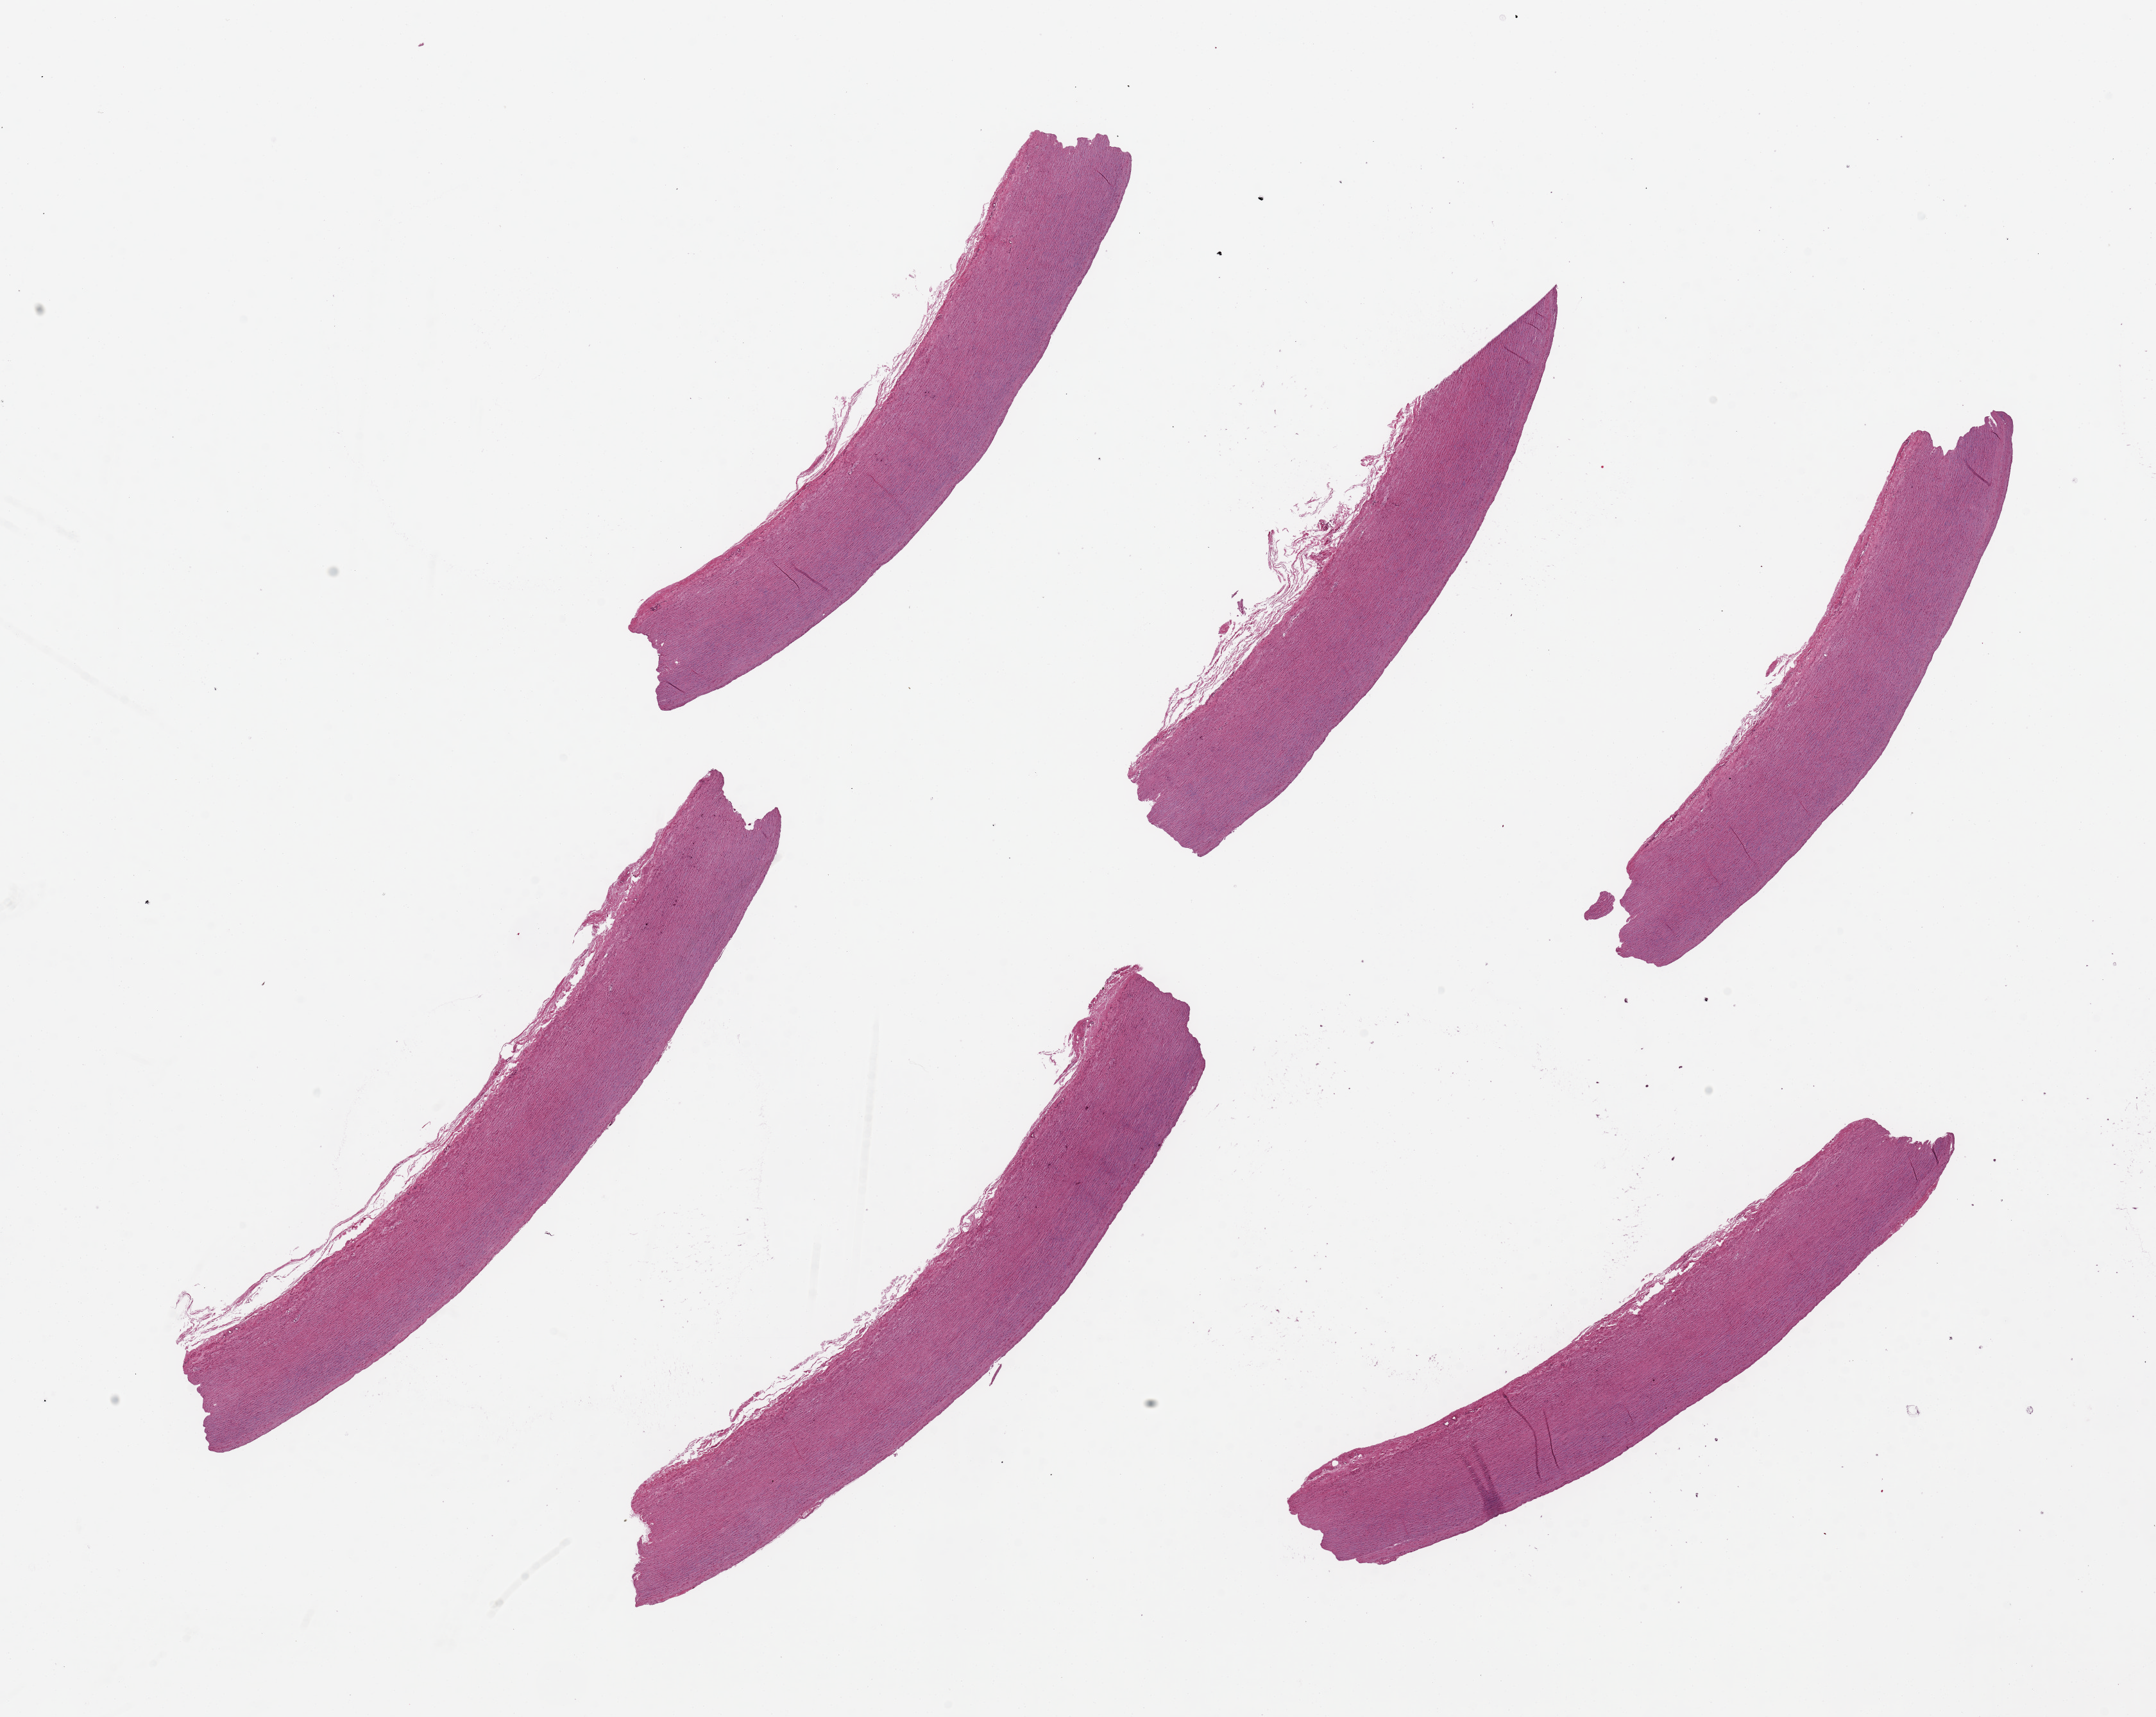
Whole-slide image, hematoxylin and eosin (H&E) stain, brightfield — a low-resolution overview of the entire scanned area, about 26.6 x 21.2 mm (slide scanned at 20x); PAXgene-fixed, paraffin-embedded tissue; target tissue: aorta; tissue donor sample.
Reviewer comment on this tissue sample: 6 pieces, up to 10.5x2mm.